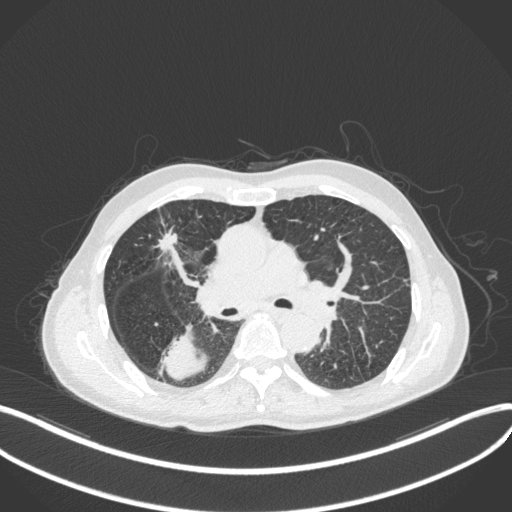
Chest CT, one axial slice. Slice 272 of 423 in the series (ordered by position). Reconstruction kernel B31f. 120 kVp. Lung window (W 1500 / L -600 HU). 1 mm slice thickness. 512 × 512 image matrix. Male patient, age 79 years. Case-level facts recorded for this patient, not image findings: clinical TNM (as recorded): T3 N0 M0.
Outlined on this slice (bounding box drawn by a radiologist):
- lung tumour (recorded histology: adenocarcinoma): bounding box [x1, y1, x2, y2] px = [157, 319, 210, 383]